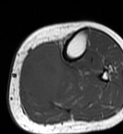
MRI of an extremity soft-tissue mass, one axial slice. Slice 24 of 68 in the series (ordered by position). MR volume resampled by the dataset authors to the PET/CT grid (not the native acquisition matrix). 123 × 134 image matrix. Female patient. From the clinical record (not read from this slice): histological type: extraskeletal high grade osteogenic sarcoma; grade: high; site of the primary tumour: left calf.
Structures marked on this image (expert contour drawn on MRI and transferred to this co-registered scan by the dataset authors):
- gross tumour volume (mass): bounding box (x1, y1, x2, y2) in pixels: (20, 43, 64, 101)